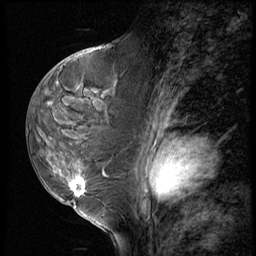
Breast MRI (dynamic contrast-enhanced), one sagittal slice; slice 32 of 60 in the series (ordered by position); 3 images stored at this slice position (order not interpretable as contrast timing); 1.5 T; TE 4.2 ms, TR 8.9 ms; 2.5 mm slice thickness; 256 × 256 image matrix. Patient: female, 50 years. Case-level facts recorded for this patient, not image findings: setting: breast cancer imaged before/during neoadjuvant chemotherapy; receptor status: HR-positive, HER2-negative.
Outlined on this slice (semi-automatically segmented with operator editing):
- analysis volume of interest (the breast-tissue region the enhancement analysis was run in; not a lesion): bounding box [x1, y1, x2, y2] px = [38, 102, 118, 213]
- tumour enhancement mask (voxels above the 140 % enhancement threshold inside the analysis volume of interest): [71, 178, 87, 195]